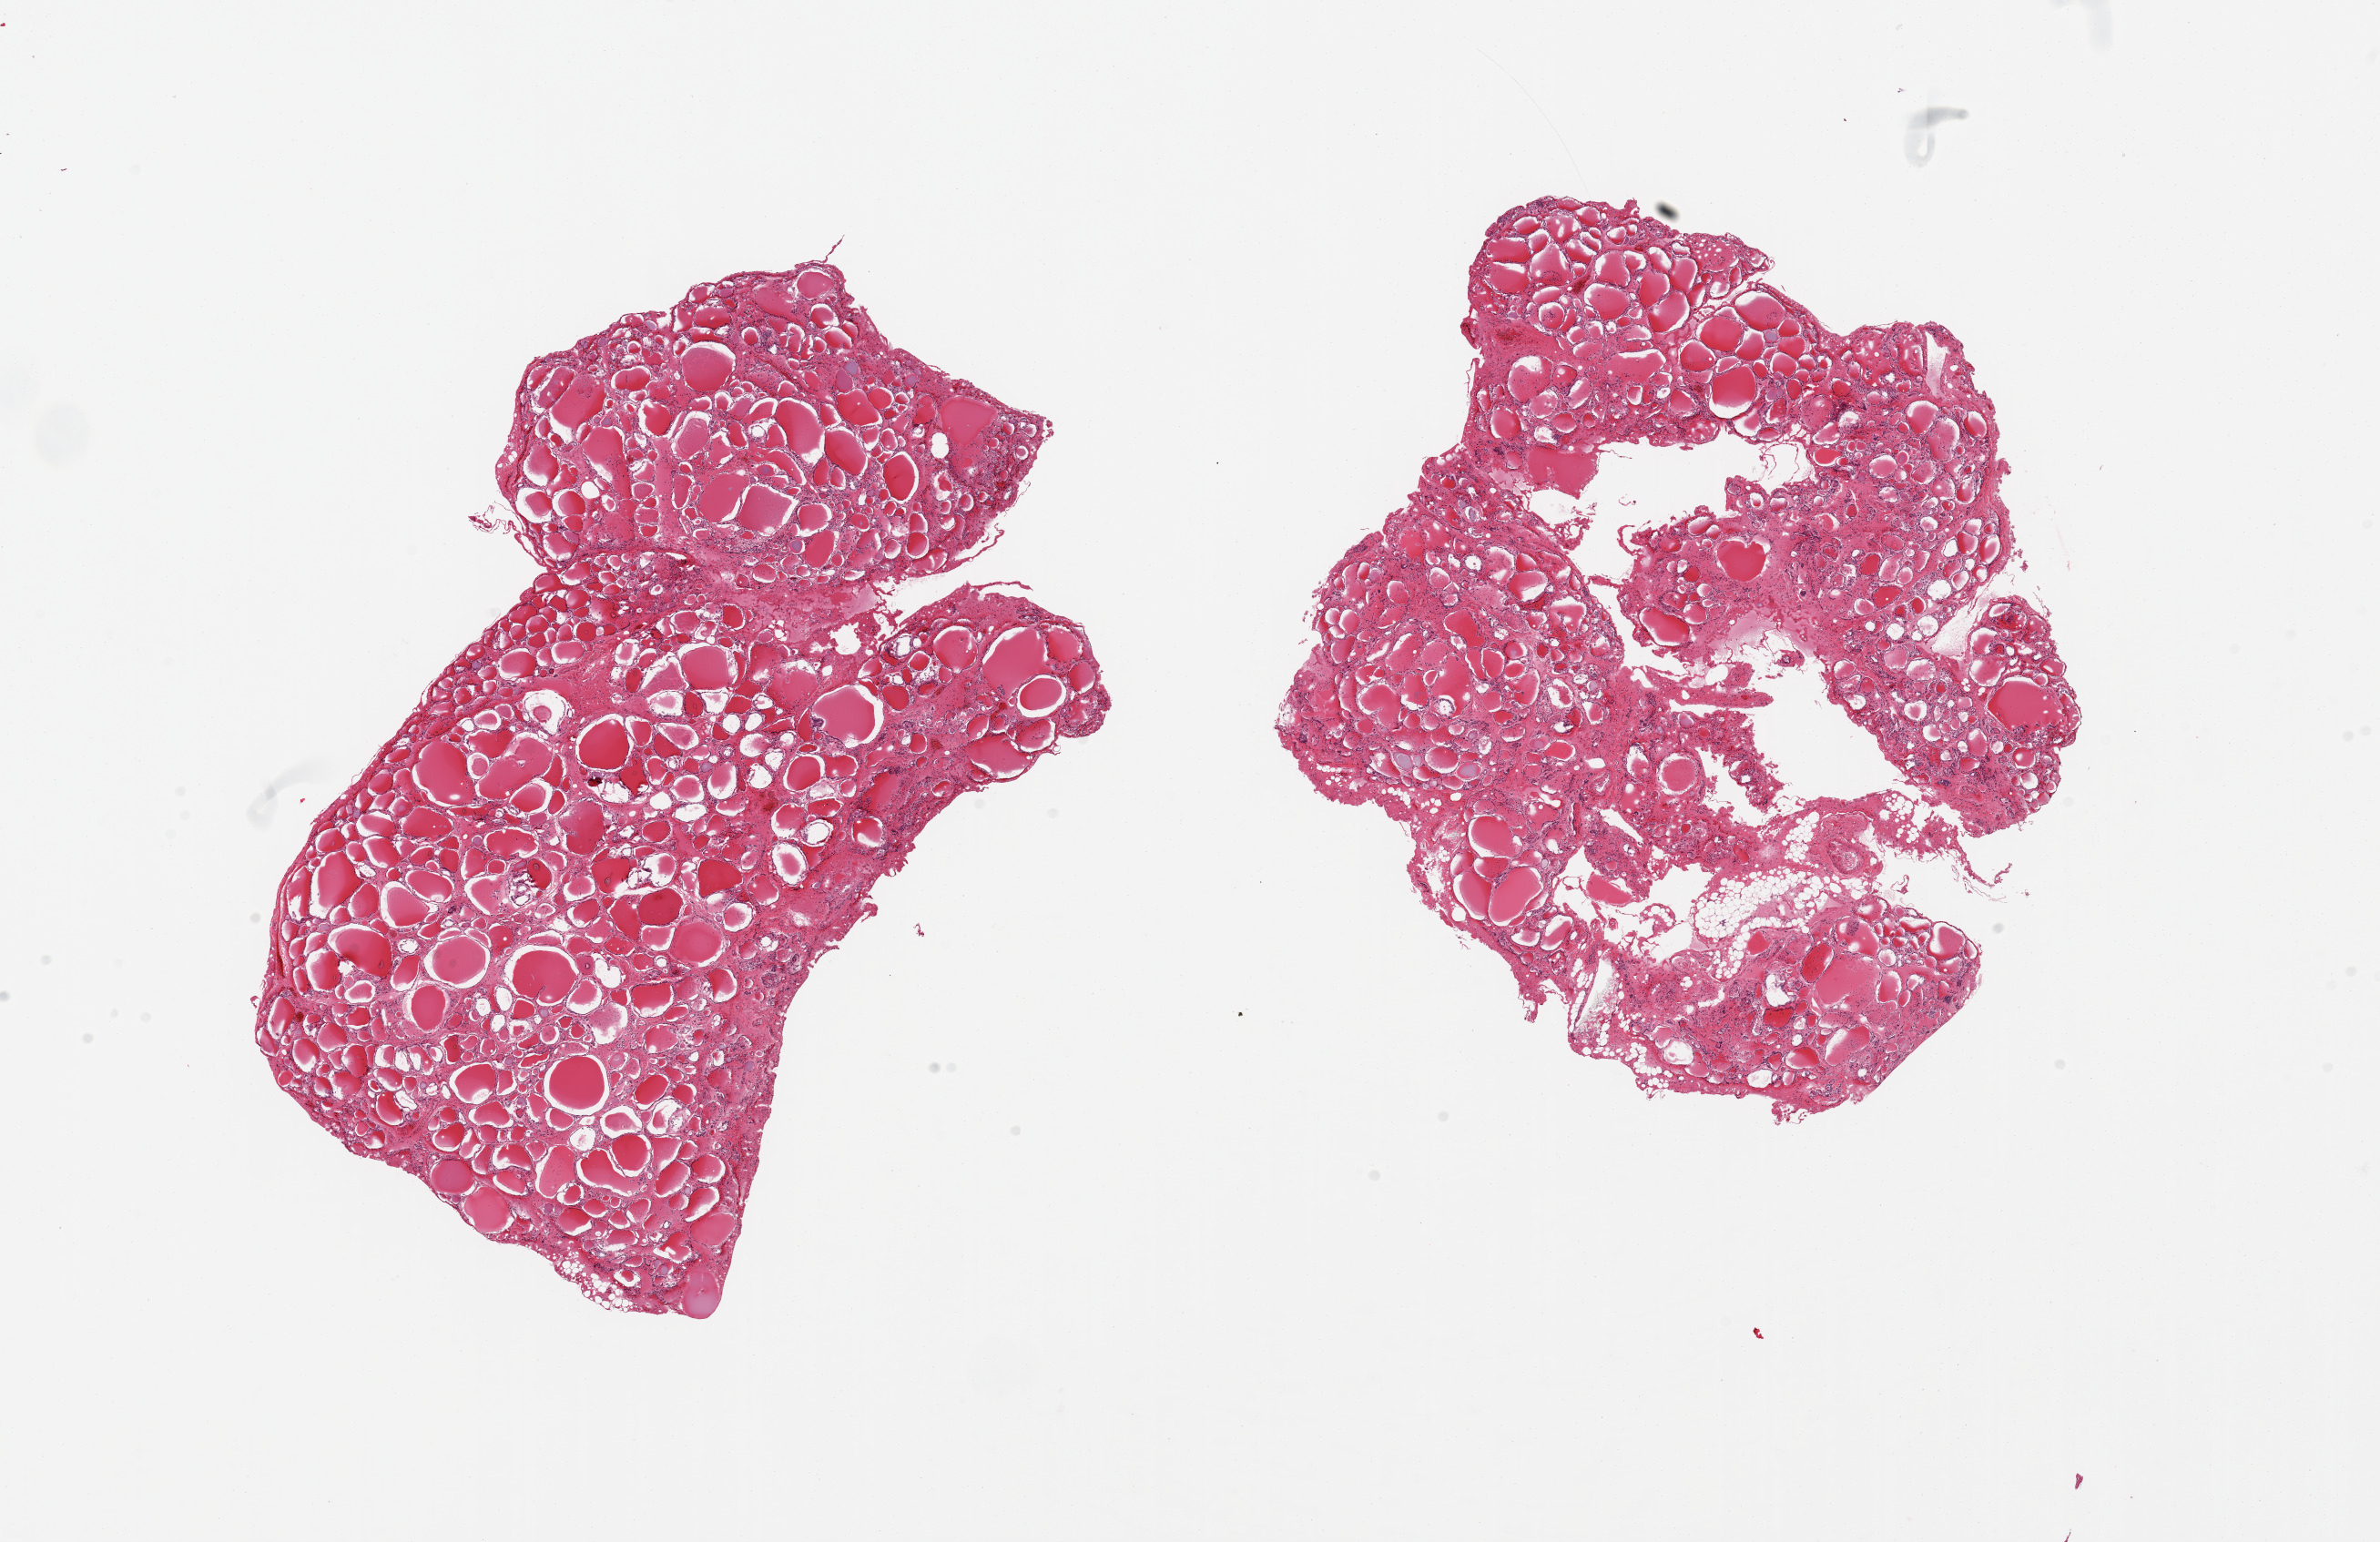
Whole-slide image, H&E stain — shown as a low-resolution overview of the whole scanned area (about 20.7 x 13.4 mm, slide scanned at 20x), PAXgene-fixed, paraffin-embedded tissue, target tissue: thyroid, tissue donor sample. Donor sex: male.
Pathologist's review note for this sample: 2 pieces; mild interstitial fibrosis.